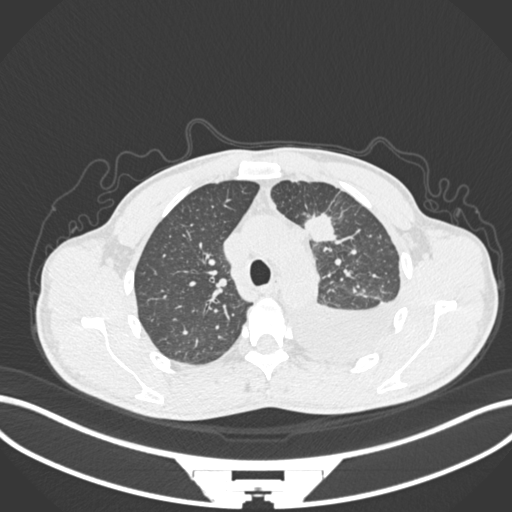
Chest CT, one axial slice; position 159 of 244 along the scan axis; 120 kVp; lung window (W 1500 / L -600 HU); 1 mm slice thickness; 512 × 512 image matrix, field of view 400 × 400 mm. Male patient, age 49 years. Case-level facts recorded for this patient, not image findings: clinical TNM (as recorded): T1c N1 M1.
Structures marked on this image (rectangle marked by the reading radiologist):
- lung tumour (recorded histology: adenocarcinoma): box from (x=307, y=211) to (x=339, y=243) px